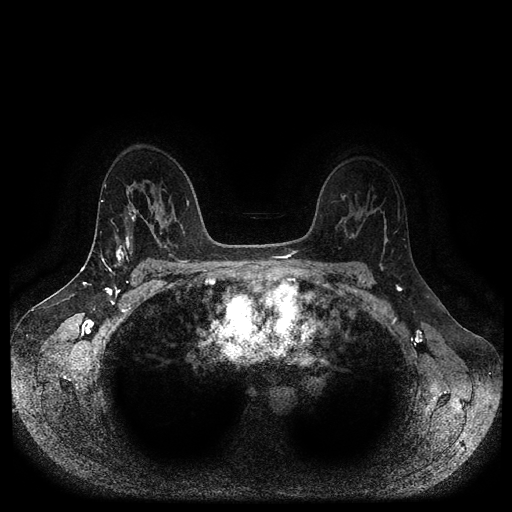
Breast MRI (dynamic contrast-enhanced, multi-phase), one axial slice; position 68 of 116 along the scan axis; dynamic contrast-enhanced series, time point 2 of 5 at this slice position (early post-contrast); 1.5 T; TE 2.6 ms, TR 5.3 ms; 2 mm slice thickness; 512 × 512 image matrix, field of view 360 × 360 mm. Female patient, age 45 years.
Annotated regions visible in this slice (semi-automatic segmentation, software-assisted and operator-edited):
- breast lesion (labelled 'tumour' in the annotation; benign lesions carry a separate 'benign' label): bounding box <115,247,124,266> (left, top, right, bottom; pixels)